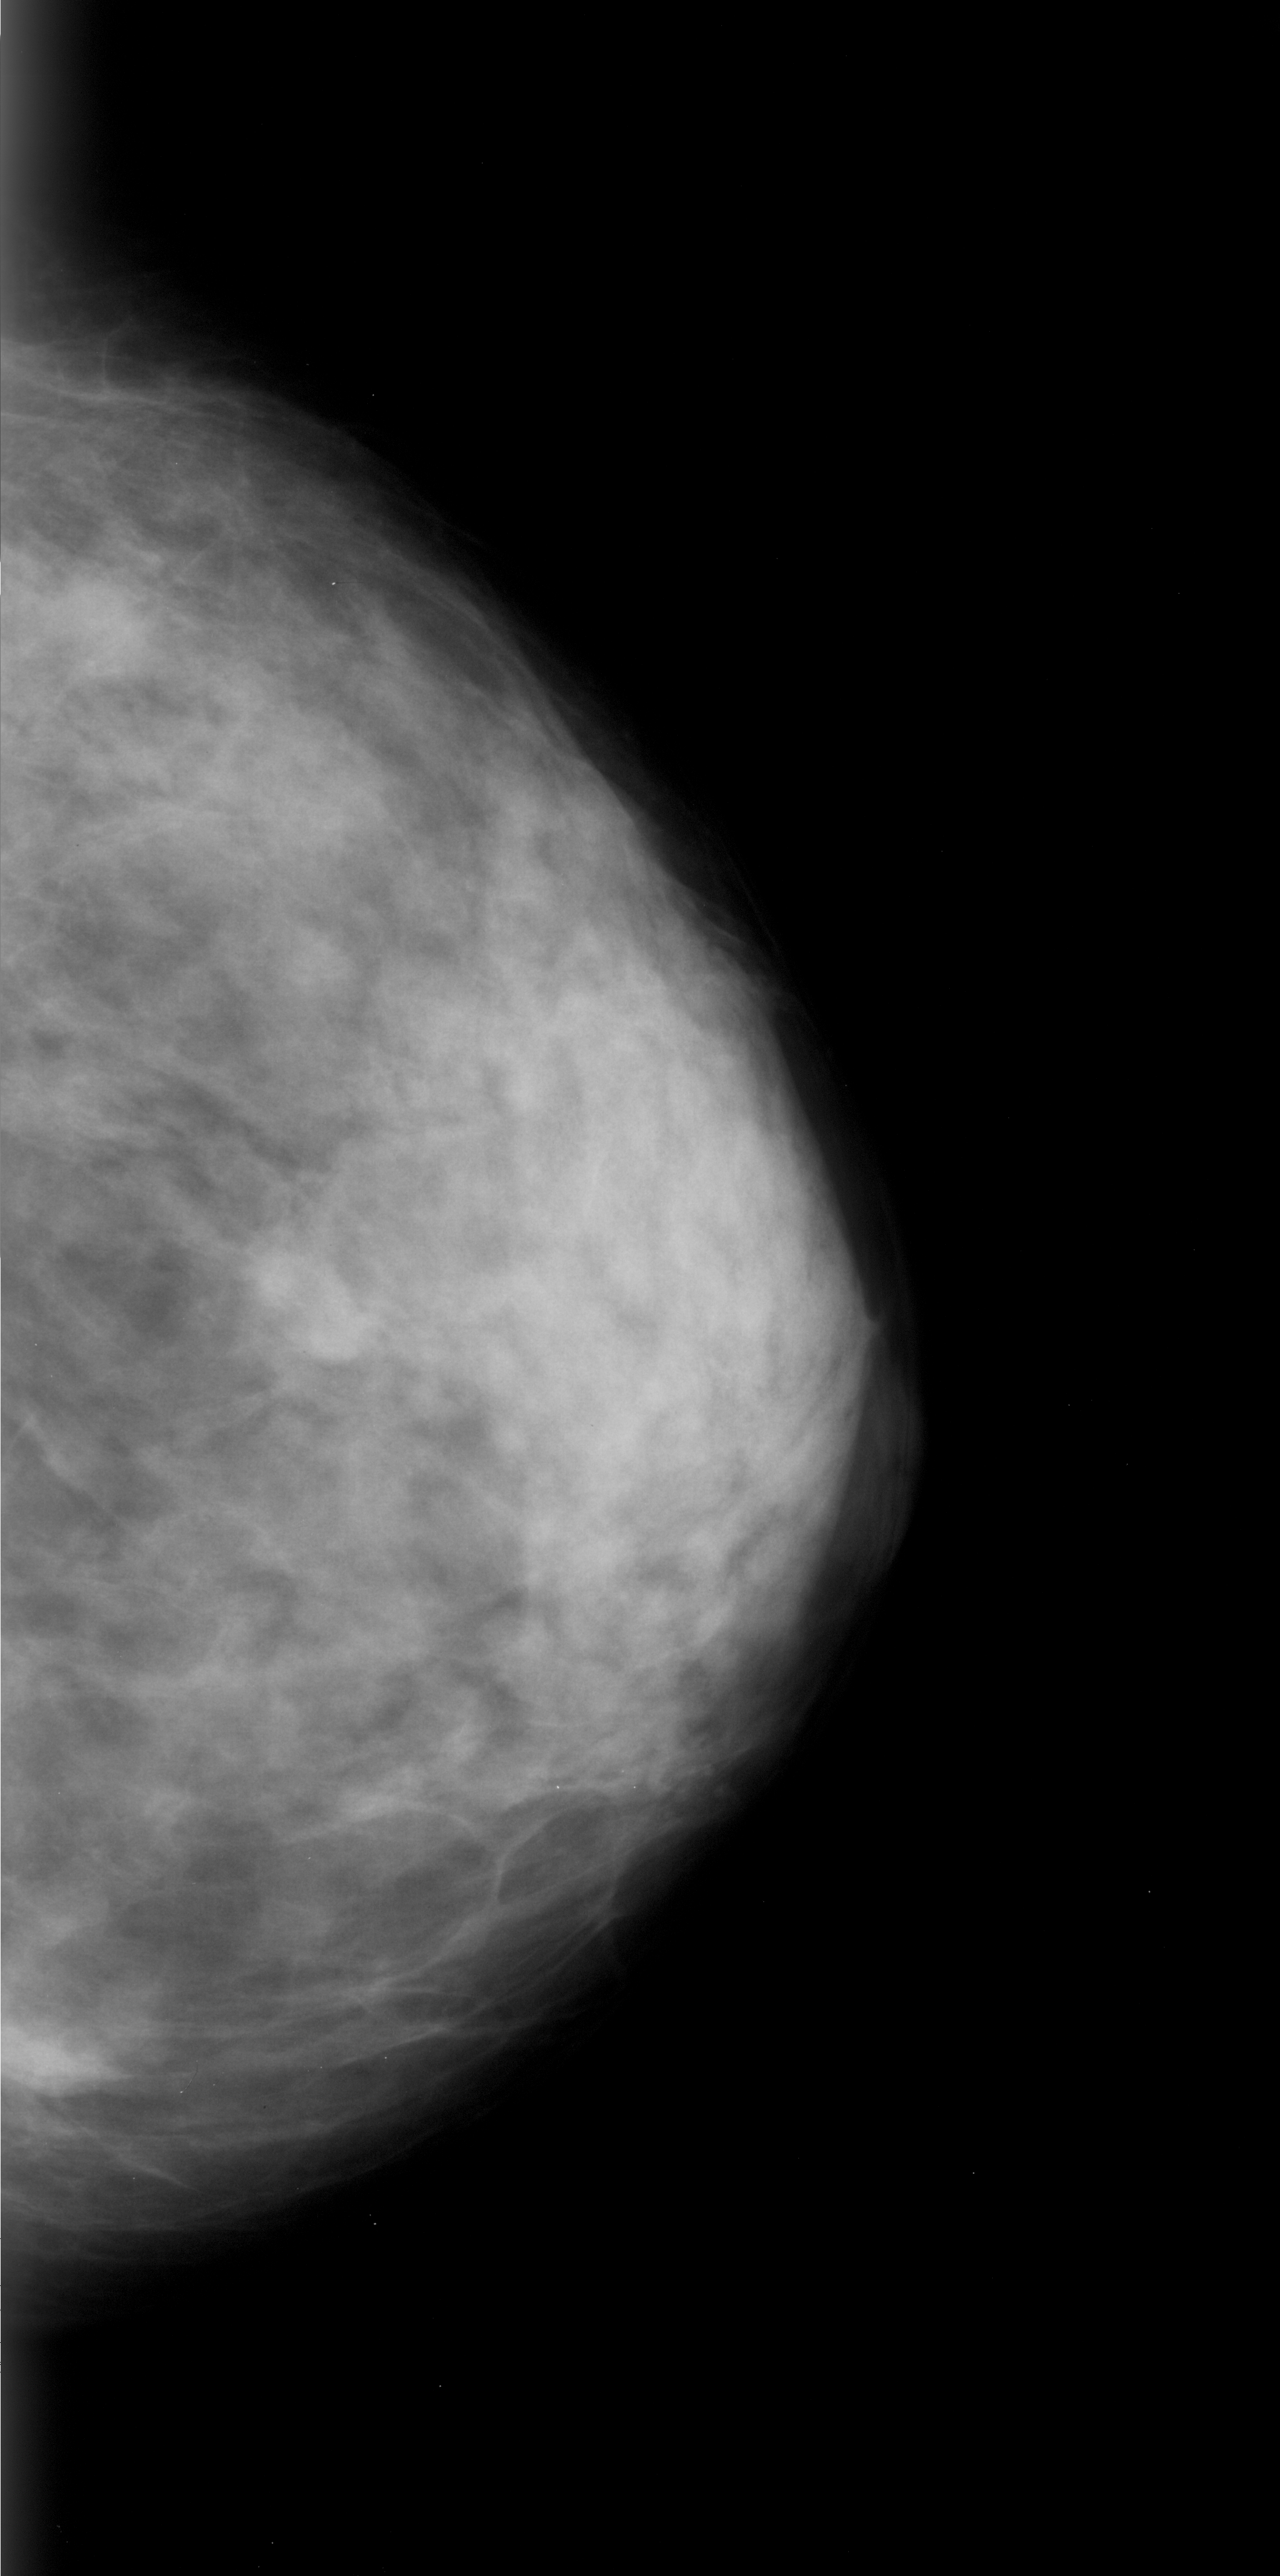
Mammogram (digitized film); right breast; CC view; breast composition: heterogeneously dense (BI-RADS density category 3 of 4).
Finding: mass, shape oval, margins ill defined; BI-RADS assessment category 4; pathology result (as recorded, not read from the image): malignant.